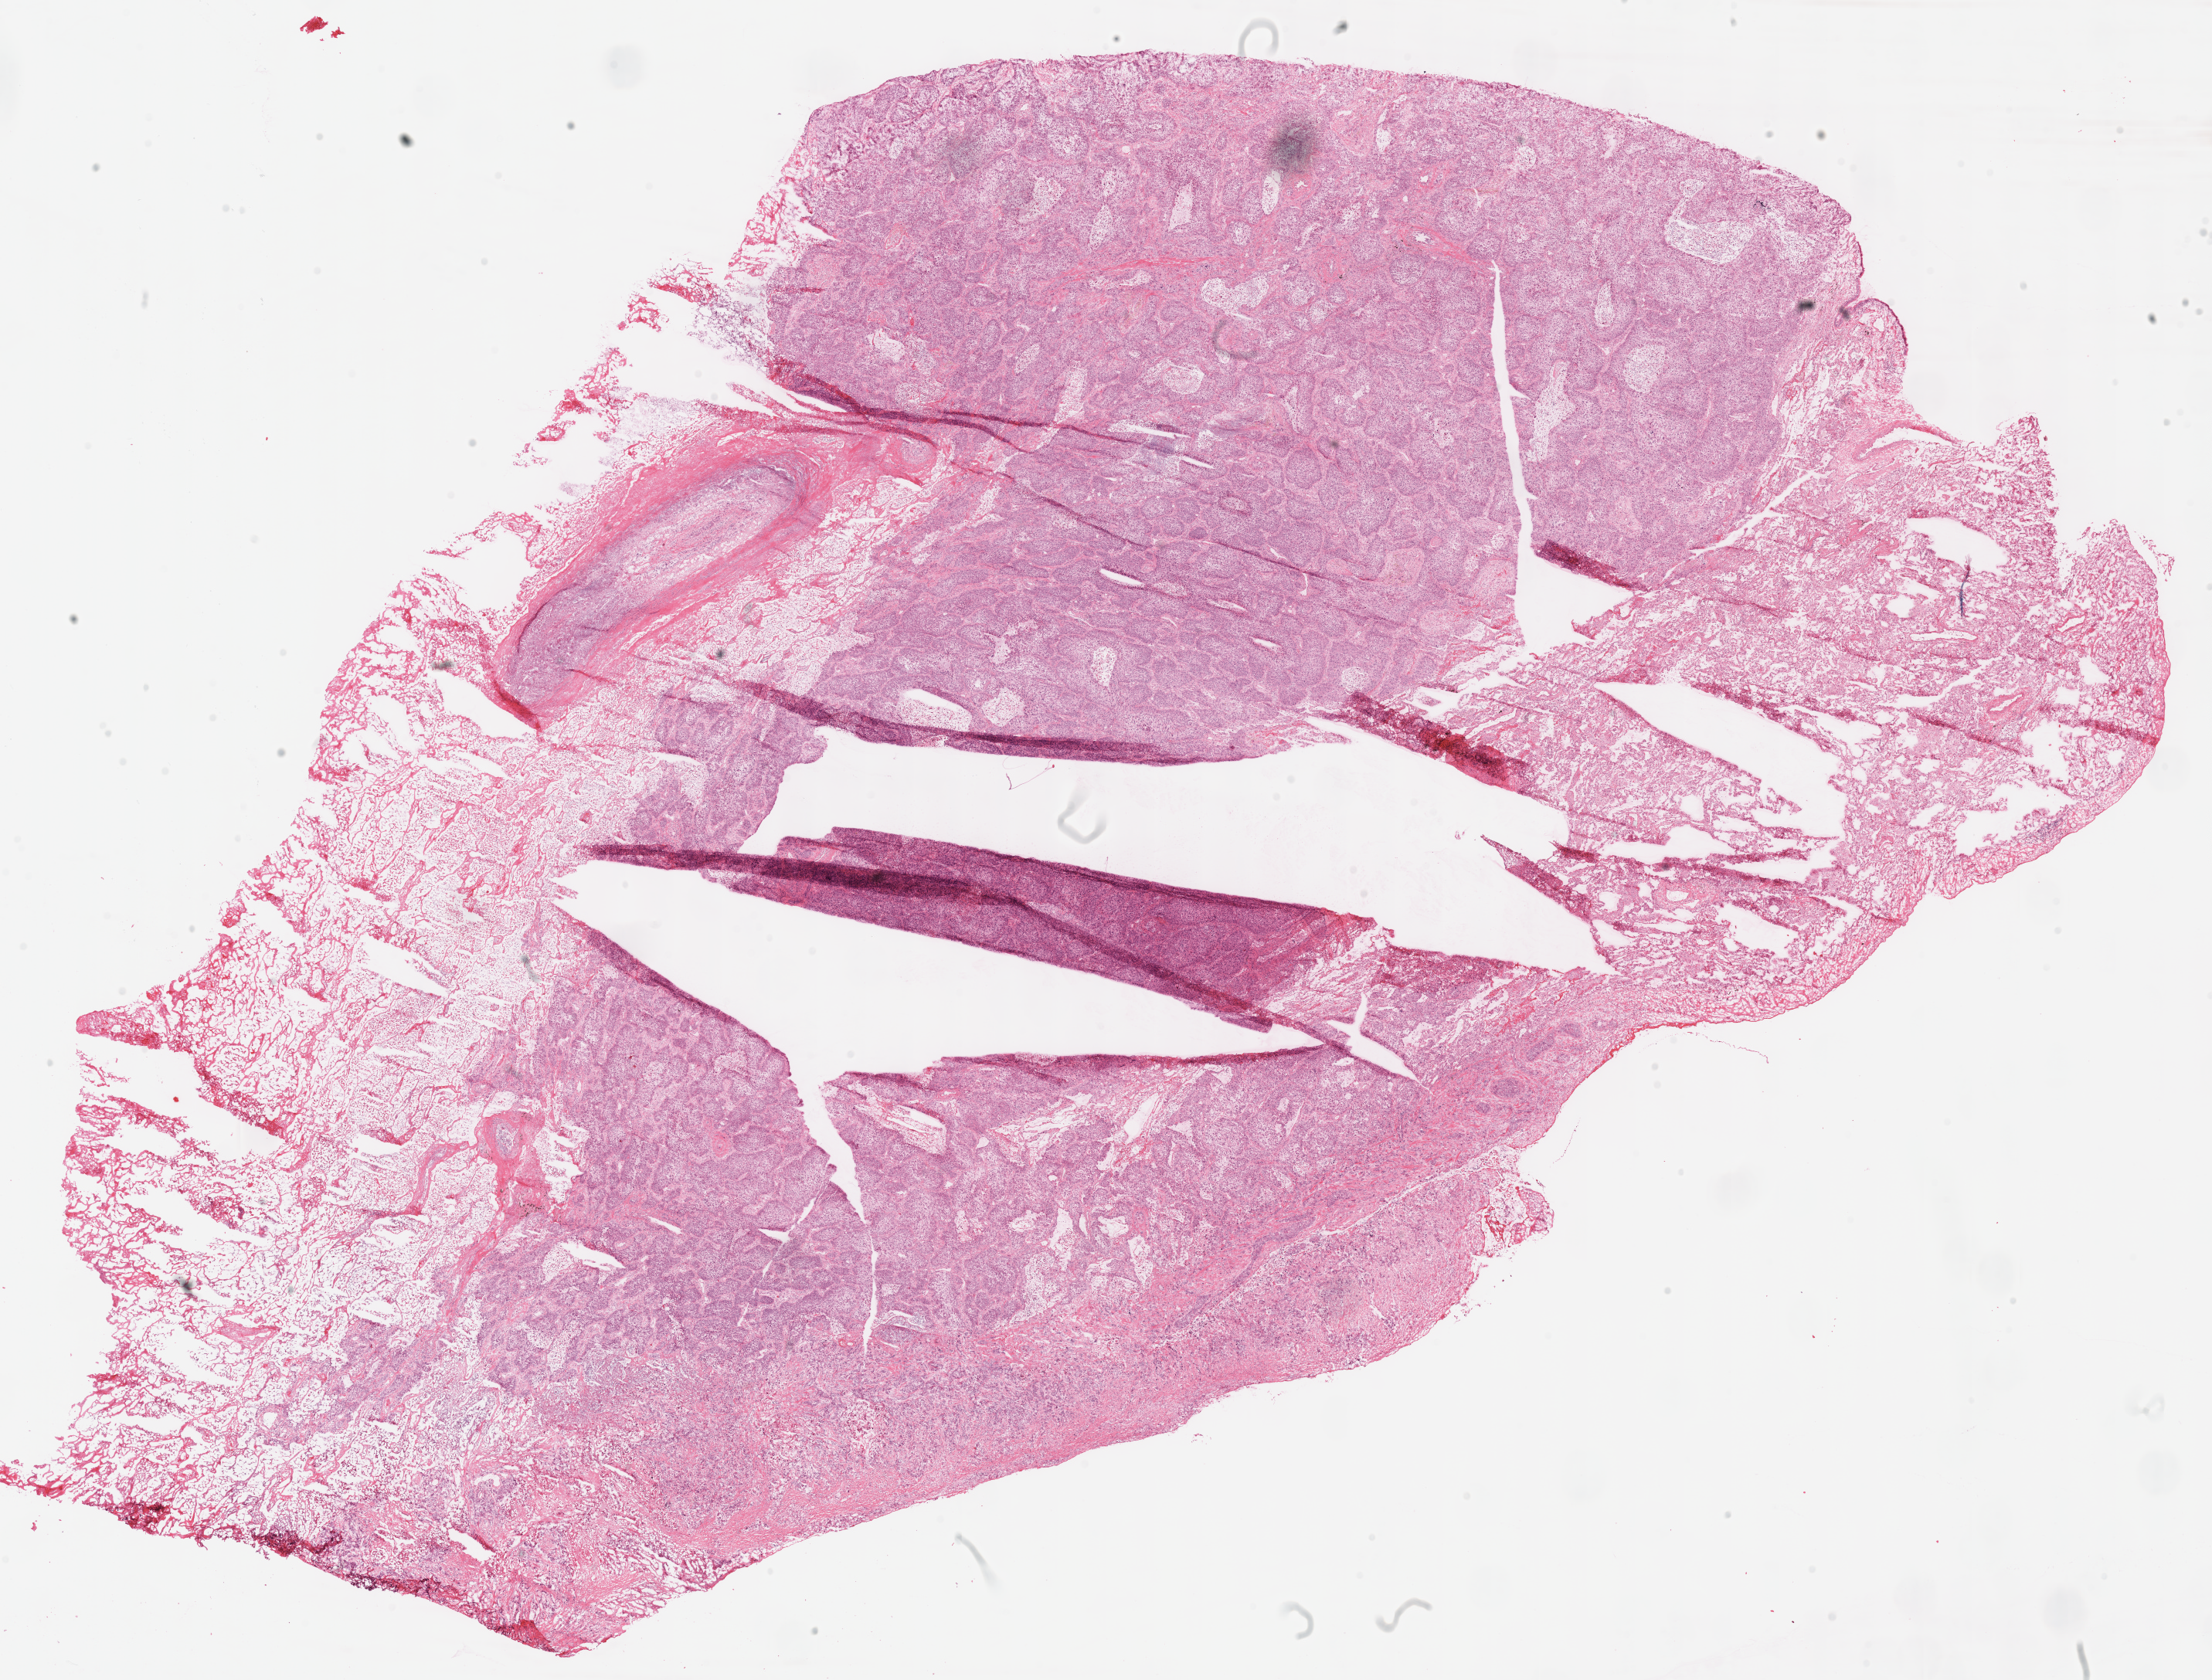
Whole-slide histology image, H&E-stained, a low-resolution overview of the entire scanned area, about 22.5 x 17.1 mm (acquisition: 40x scan), frozen section from the top of the tissue portion, sample: primary tumour, lung. Male, age 72 years at initial diagnosis. Slide review estimates, as recorded: tumour cells 65%, tumour nuclei 75%, normal cells 10%, stromal cells 10%, necrosis 15%.
• AJCC pathologic stage: IIA (7th edition)
• laterality: right
• TNM: T2a N1 M0
• diagnosis: Squamous cell carcinoma, NOS (lower lobe, lung)